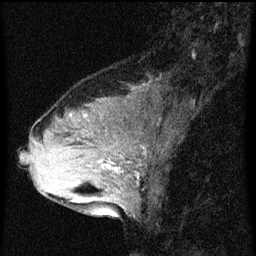
Breast MRI (dynamic contrast-enhanced), one sagittal slice; slice 25 of 60 in the series (ordered by position); dynamic contrast-enhanced series, image 2 of 3 at this slice position (ordered by acquisition); 1.5 T; TE 4.2 ms, TR 8 ms; 2 mm slice thickness; 256 × 256 image matrix, field of view 180 × 180 mm. Patient: female, 33 years.
Outlined on this slice (semi-automatically segmented with operator editing):
- analysis volume of interest (the breast-tissue region the enhancement analysis was run in; not a lesion): bounding box (x1, y1, x2, y2) in pixels: (61, 126, 148, 213)
- tumour enhancement mask (voxels above the 70 % enhancement threshold inside the analysis volume of interest): (99, 160, 121, 173)